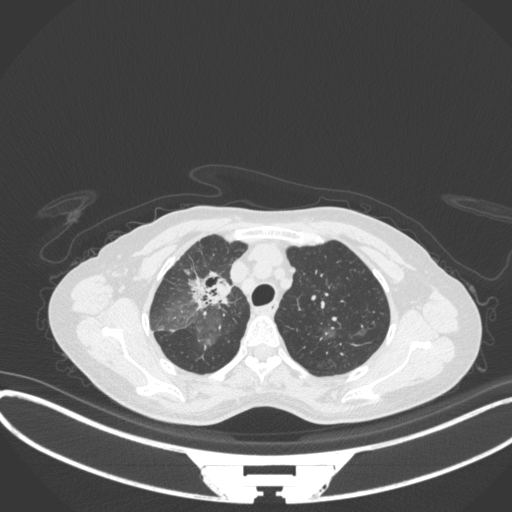
Chest CT, one axial slice; slice 249 of 311 in the series (ordered by position); reconstruction kernel B31f; lung window (W 1500 / L -600 HU); 1 mm slice thickness; 512 × 512 image matrix. Female patient, age 59 years. Case-level facts recorded for this patient, not image findings: clinical TNM (as recorded): T3 N0 M0; histopathological grade: G1.
Outlined on this slice (rectangle marked by the reading radiologist):
- lung tumour (recorded histology: adenocarcinoma): bounding box (x1, y1, x2, y2) in pixels: (182, 266, 233, 314)